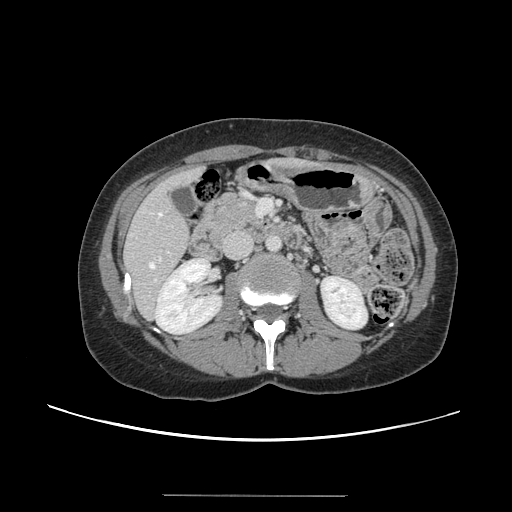
Contrast-enhanced abdominal CT, one axial slice; slice 54 of 144 in the series (ordered by position); 120 kVp; intravenous contrast given; soft-tissue window (W 400 / L 40 HU); 2.5 mm slice thickness; 512 × 512 image matrix, field of view 380 × 380 mm. Female patient, age 53 years. From the clinical record (not read from this slice): diagnosis: colorectal cancer liver metastases, imaged before liver resection; multiple liver metastases: yes; largest metastasis: 1.1 cm; disease in both lobes: no.
Structures marked on this image (expert manual segmentation):
- hepatic veins: bounding box [x1, y1, x2, y2] px = [149, 212, 162, 268]
- liver: [125, 160, 308, 317]
- planned liver remnant (the part of the liver to remain after resection): [125, 160, 305, 313]
- portal vein (with intrahepatic branches): [154, 251, 170, 282]